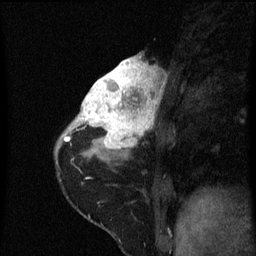
Breast MRI (dynamic contrast-enhanced), one sagittal slice. Slice 23 of 60 in the series (ordered by position). Dynamic contrast-enhanced series, image 2 of 3 at this slice position (ordered by acquisition). 1.5 T. TE 4.2 ms, TR 8 ms. 2 mm slice thickness. 256 × 256 image matrix, field of view 180 × 180 mm. Female patient, age 38 years.
Outlined on this slice (semi-automatic segmentation, software-assisted and operator-edited):
- analysis volume of interest (the breast-tissue region the enhancement analysis was run in; not a lesion): bounding box (x1, y1, x2, y2) in pixels: (80, 56, 165, 151)
- tumour enhancement mask (voxels above the 70 % enhancement threshold inside the analysis volume of interest): (80, 56, 161, 149)